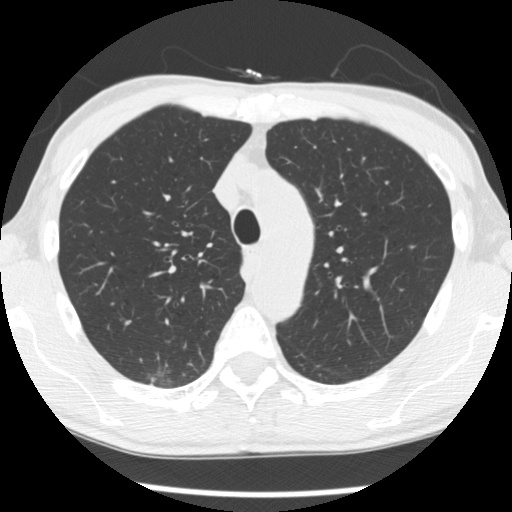
Low-dose screening chest CT, axial slice. Baseline screening round. Lung window (W 1500 / L -600 HU). 512 × 512 image matrix. Male, age 66 years at enrolment.
Expert-annotated lung lesion, bounding box [x1, y1, x2, y2] px = [135, 356, 186, 394]. The screening reader recorded 4 non-calcified nodules or masses ≥4 mm on this exam (right upper lobe, right upper lobe, right upper lobe, left lower lobe); which of them this box marks is not recorded.